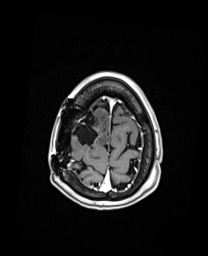
Brain MRI from a brain-tumour surgery series, one axial slice. Slice 33 of 192 in the series (ordered by position). T1-weighted post-contrast. 208 × 256 image matrix. From the clinical record (not read from this slice): histopathology: Oligodendroglioma; WHO grade: 3; IDH mutation: yes.
Structures marked on this image (manually delineated by an expert):
- previous resection cavity: bounding box (x1, y1, x2, y2) in pixels: (72, 111, 99, 144)